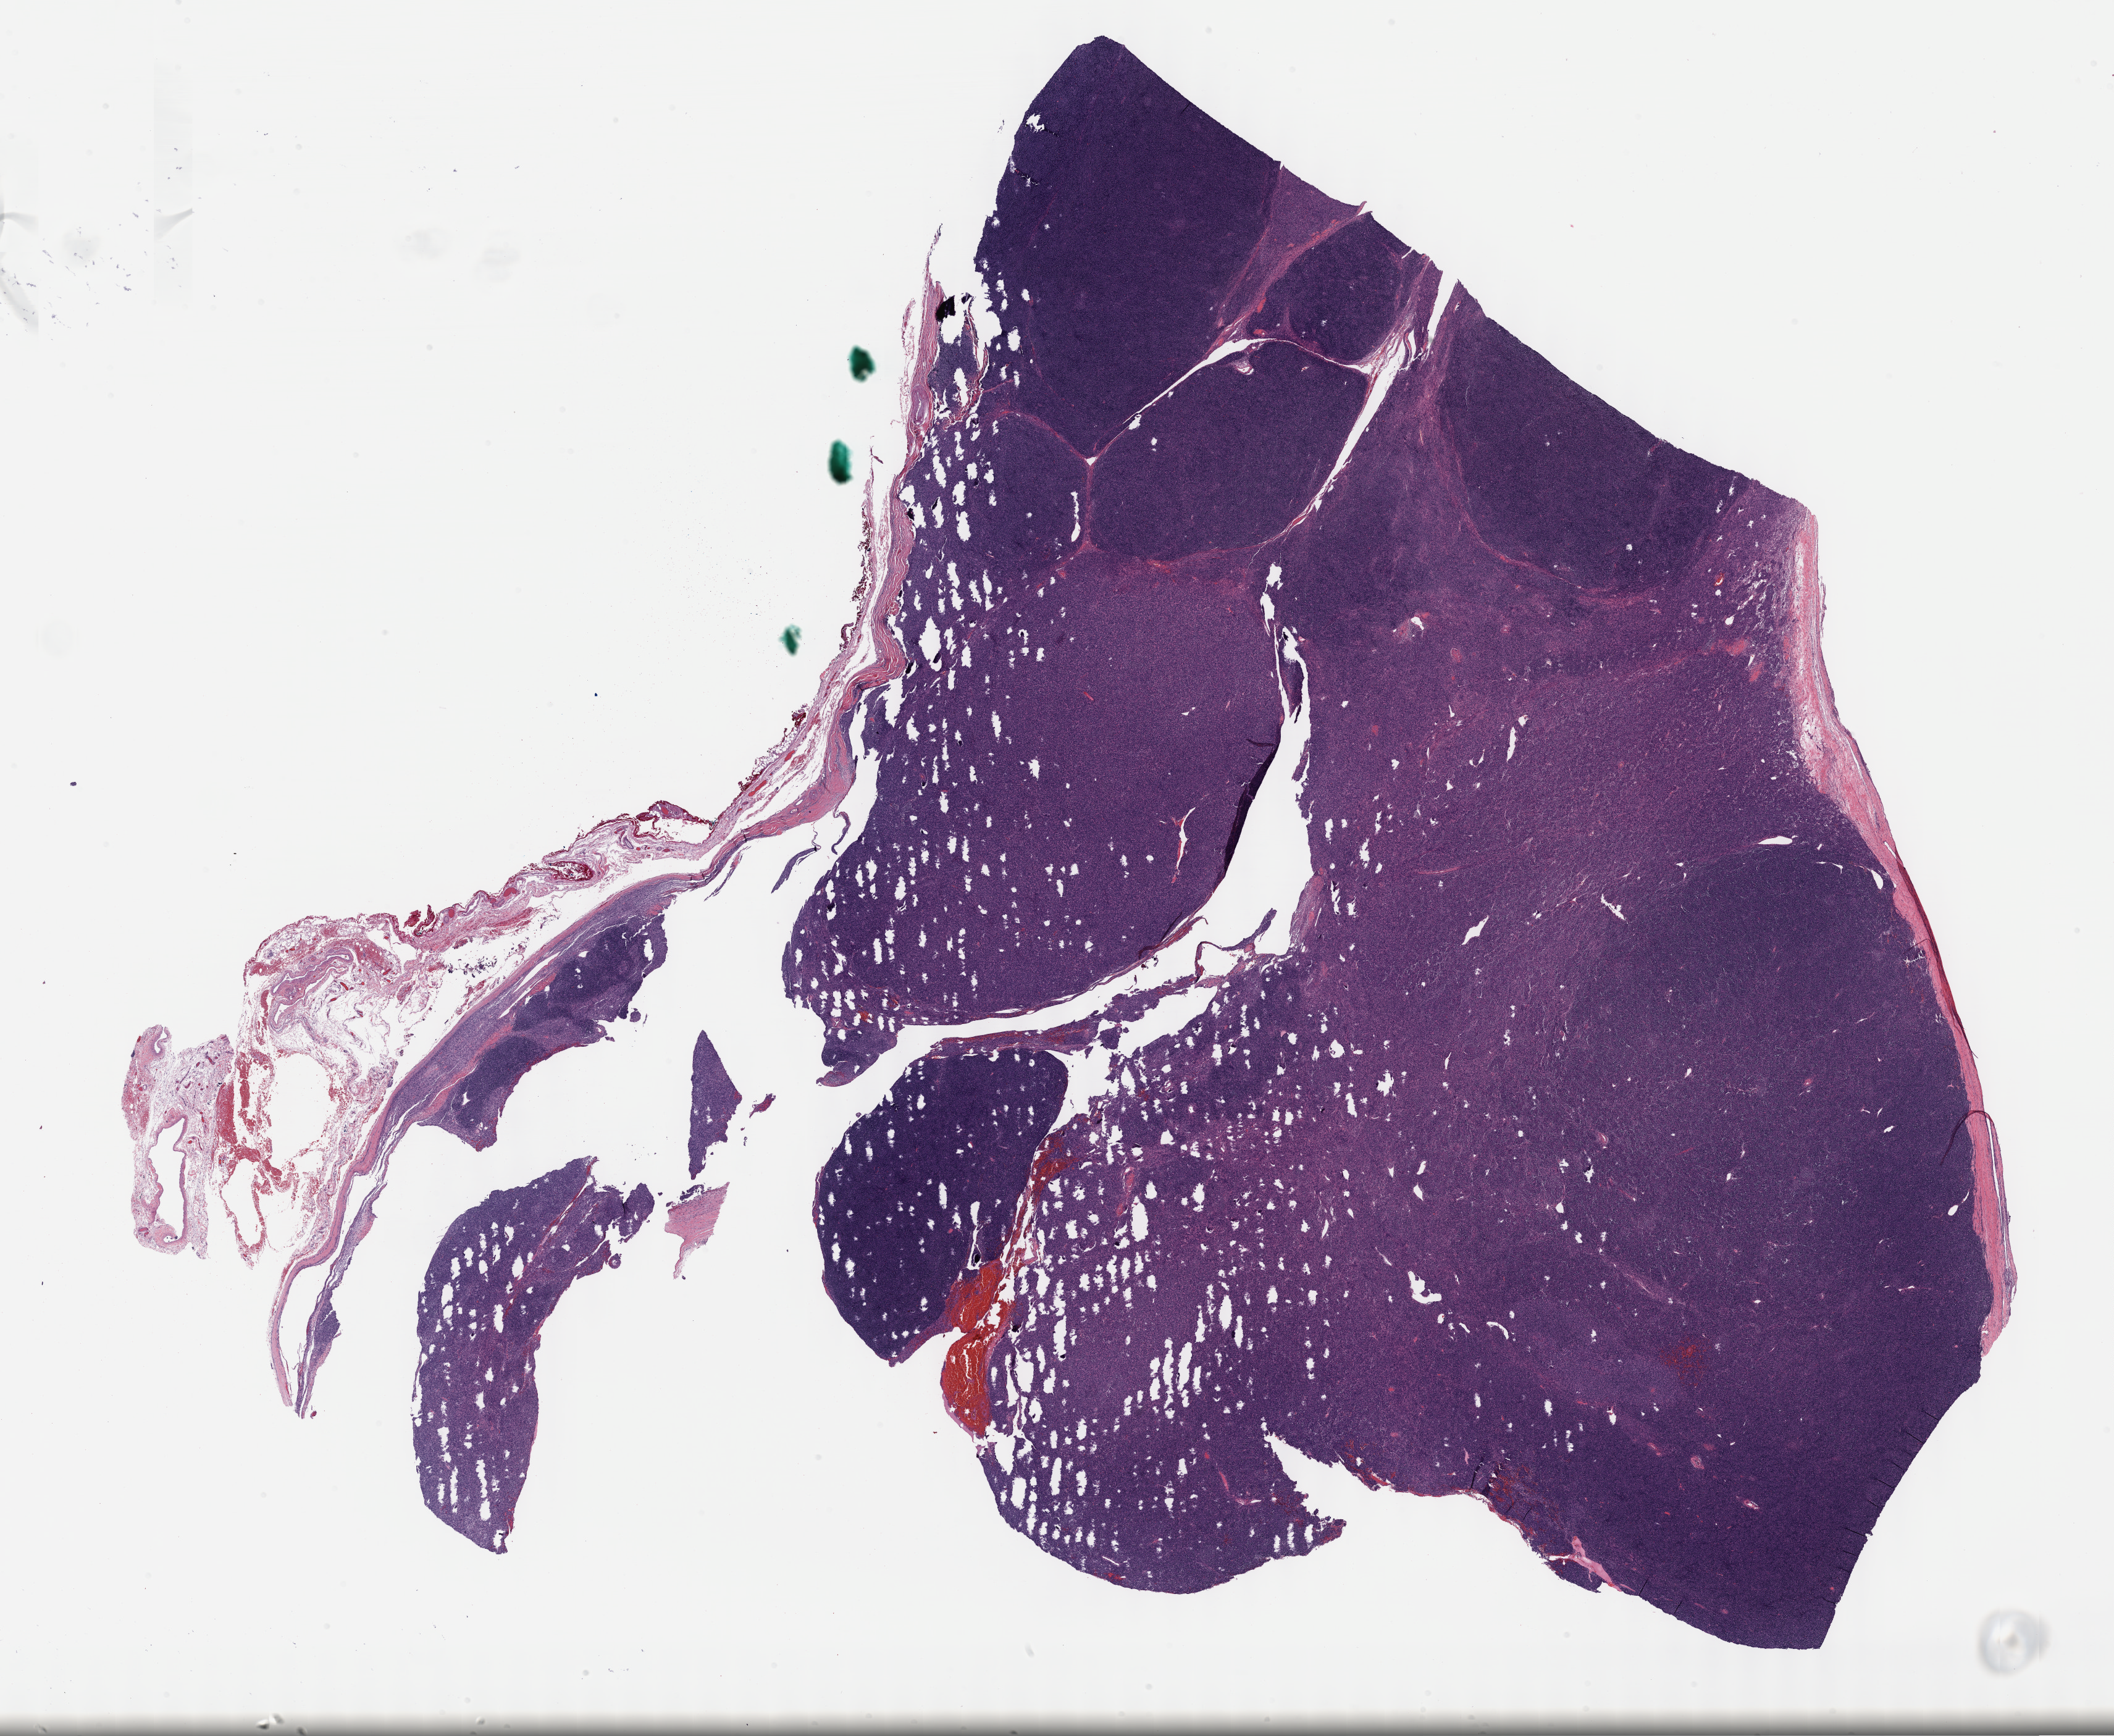
Hematoxylin and eosin (H&E) stained whole-slide image, a low-resolution overview of the entire scanned area, about 27.7 x 22.7 mm (slide scanned at 40x); formalin-fixed paraffin-embedded (FFPE) diagnostic section; sample: primary tumour, thymus. Male, age 67 years at initial diagnosis.
Diagnosis: Thymoma, type AB, NOS.